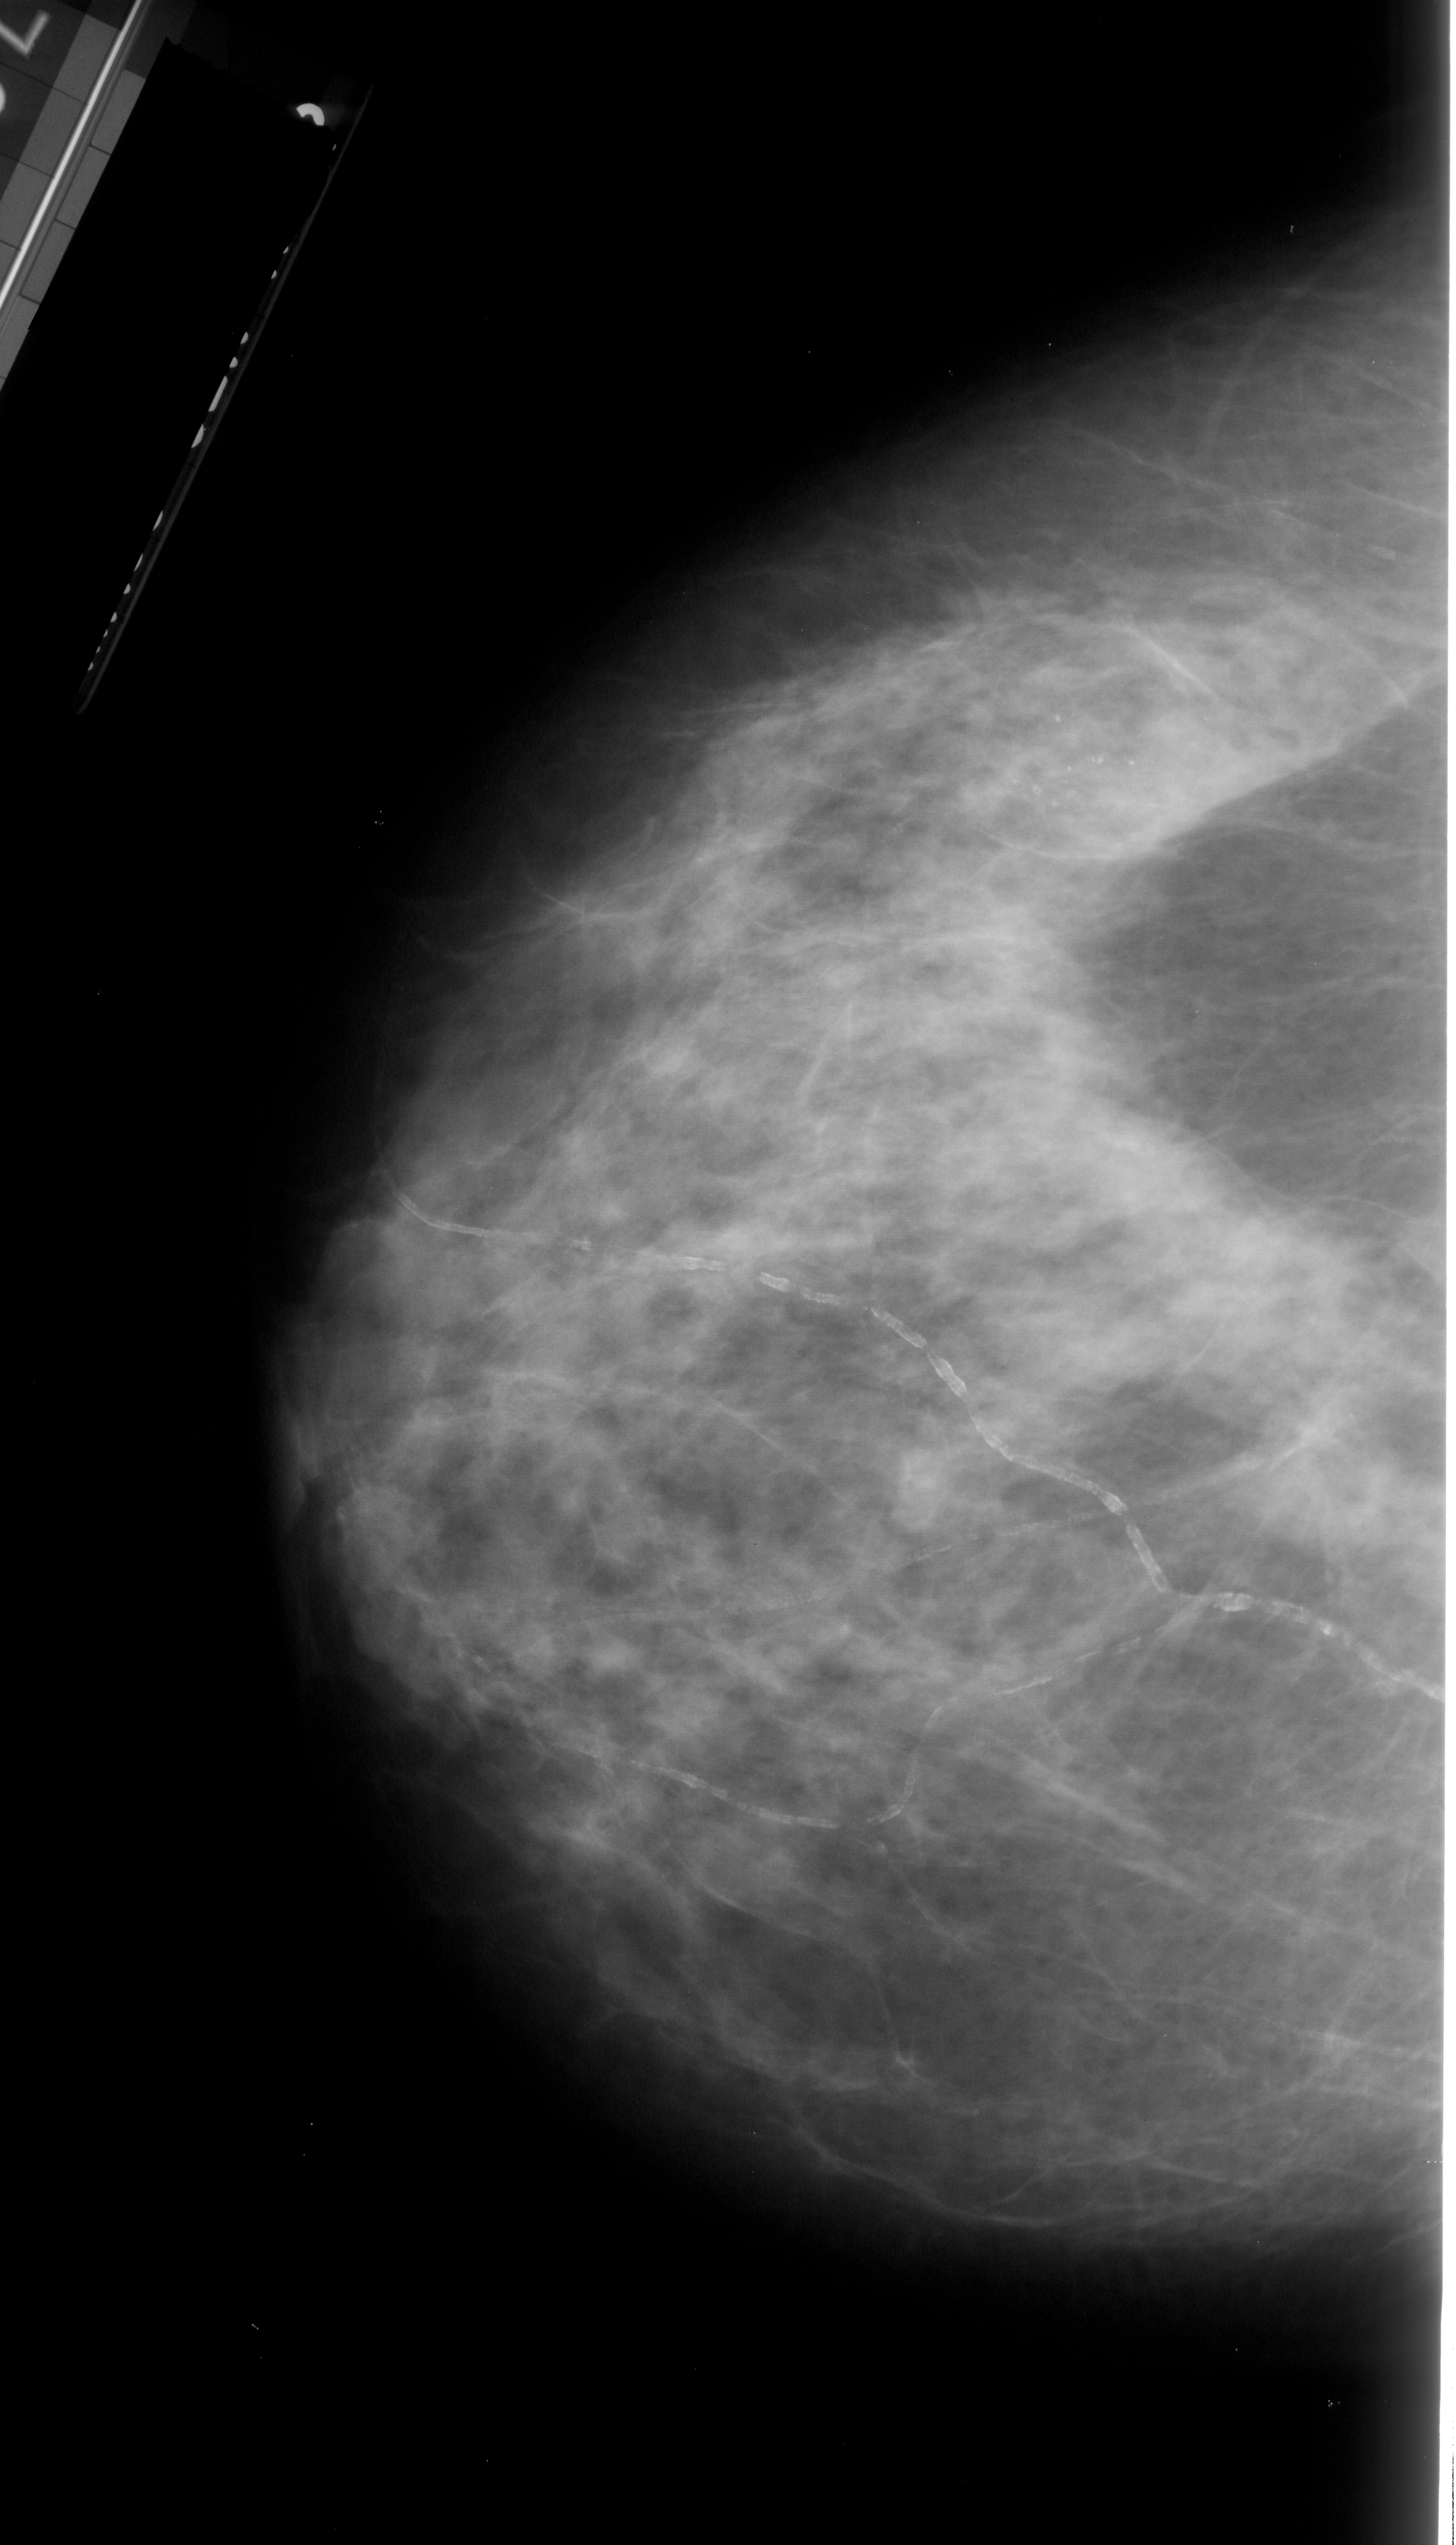
Scanned film-screen mammogram, left breast, CC view, BI-RADS breast density category 3 (scale 1–4).
Finding: calcifications, morphology pleomorphic, distribution linear; BI-RADS assessment category 4; subtlety rating 3 on a 1 (subtle) to 5 (obvious) scale; pathology result (as recorded, not read from the image): malignant.